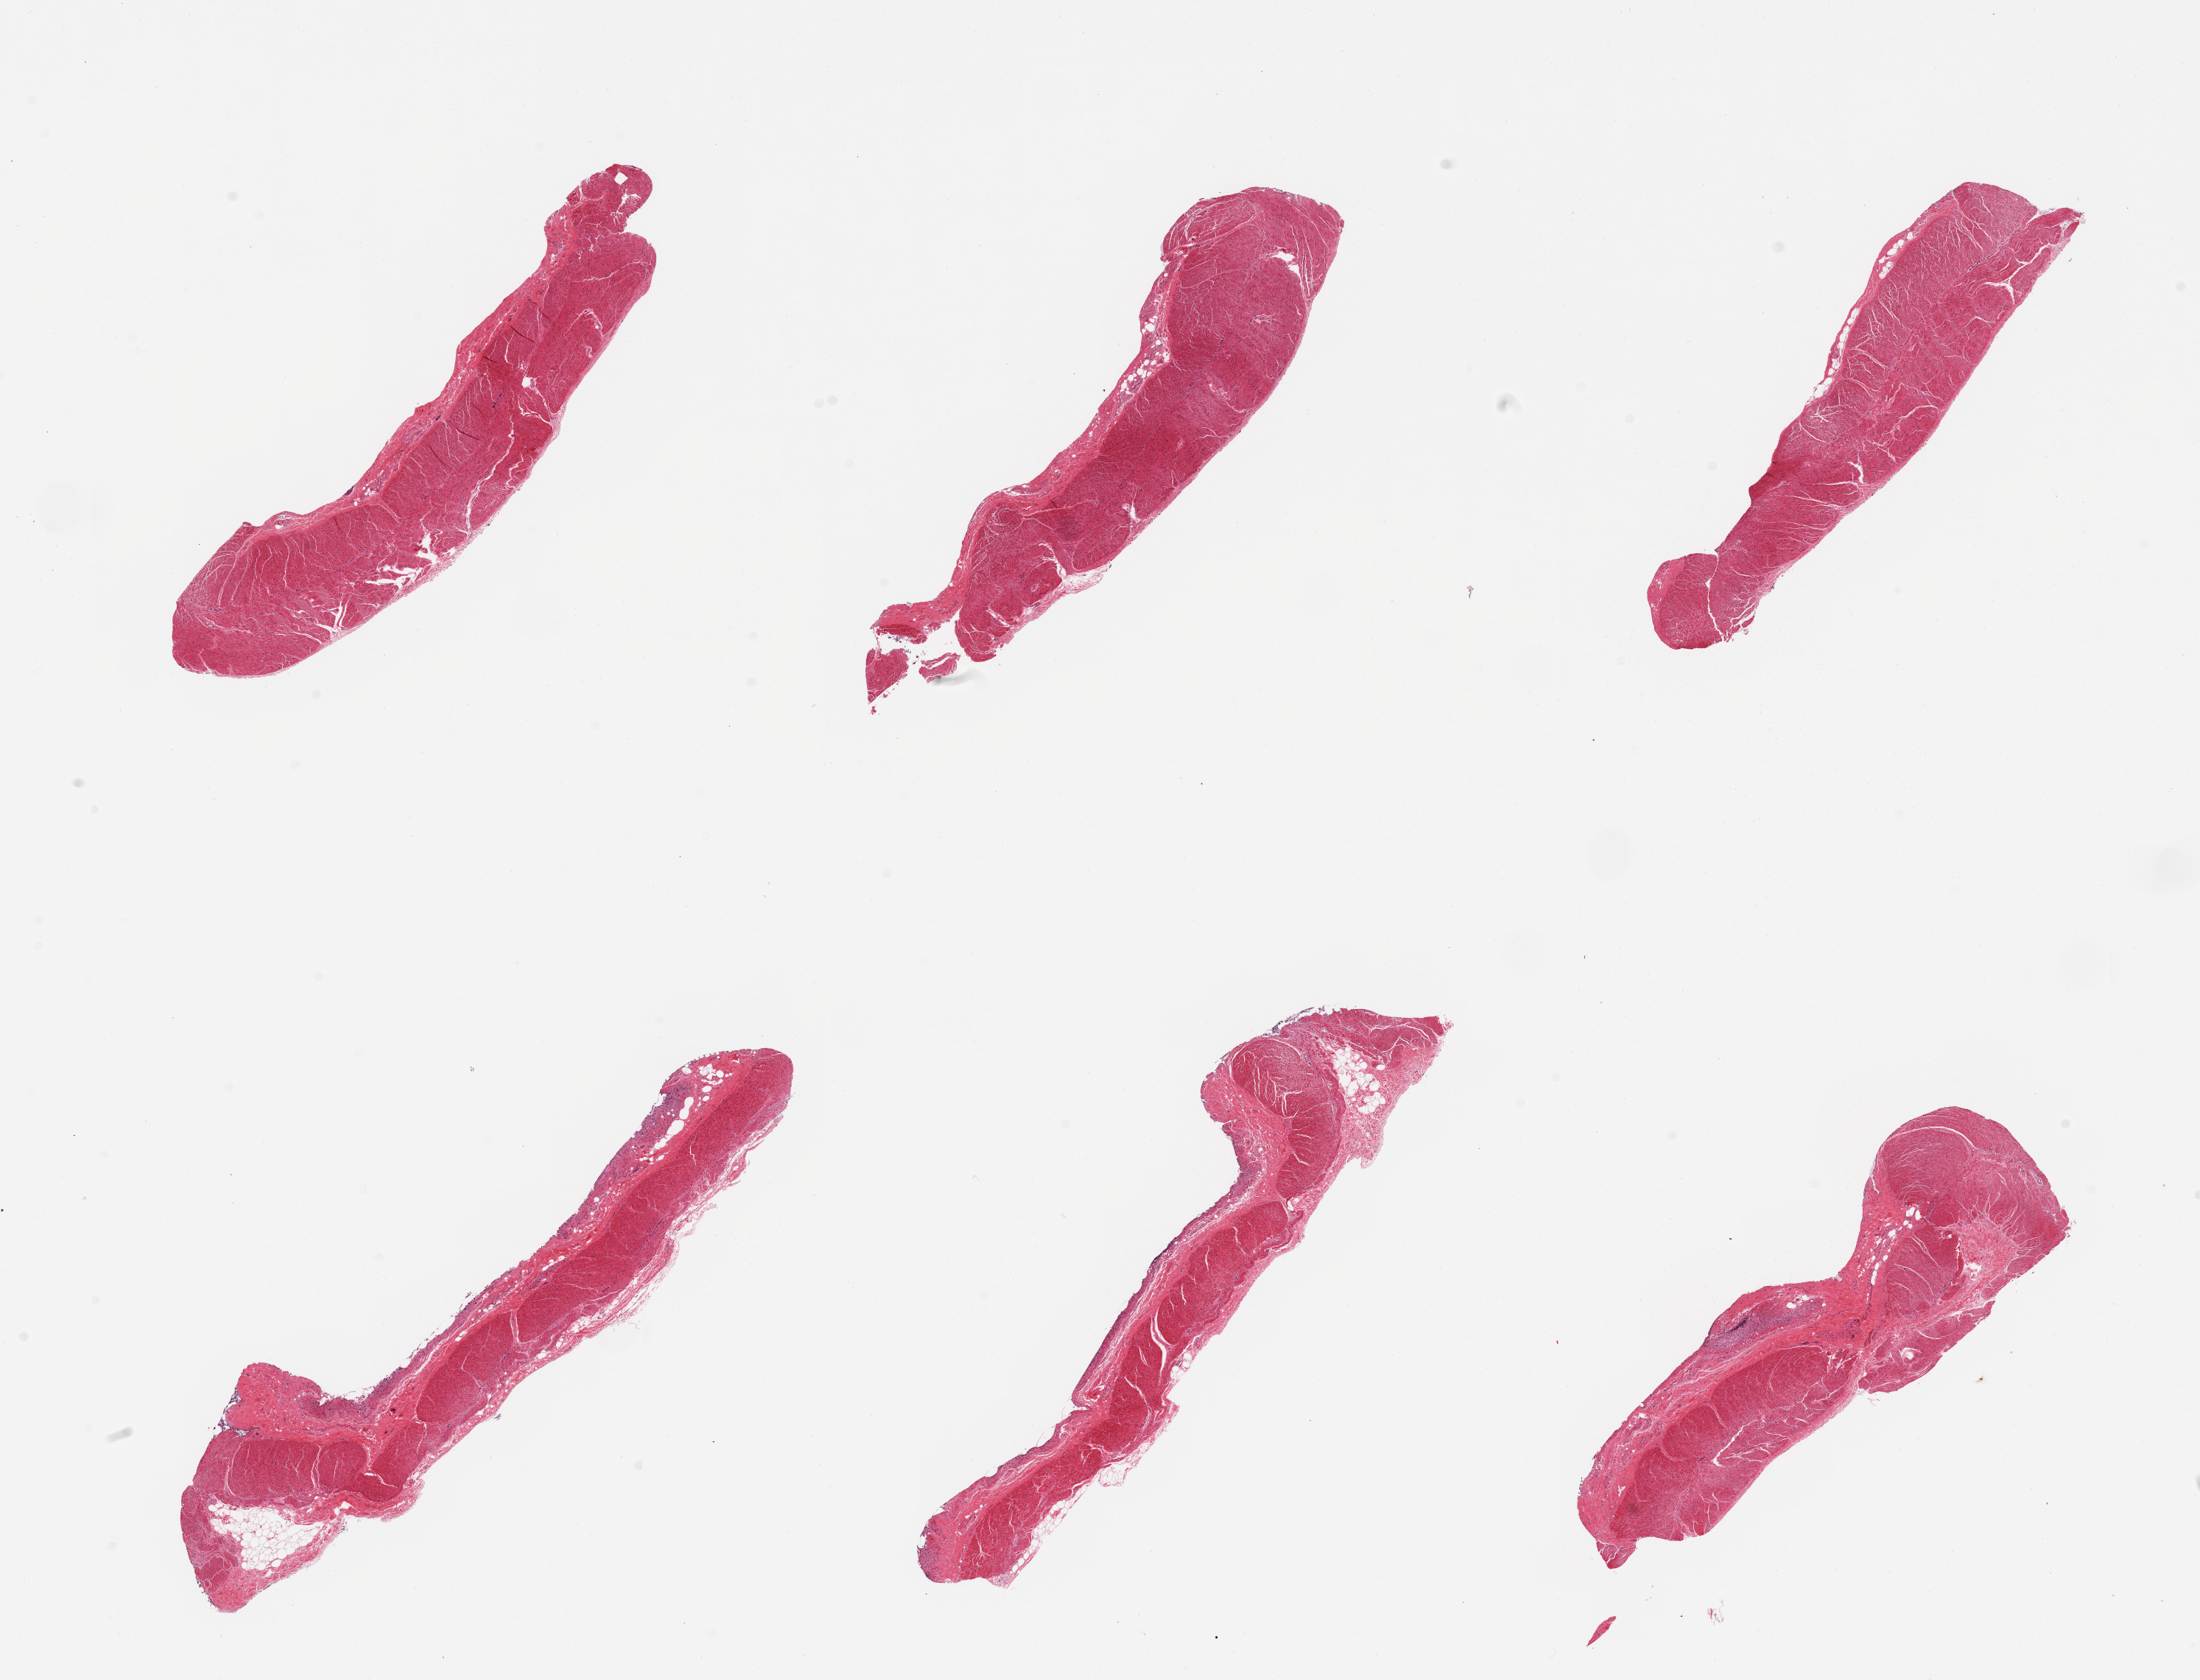
Hematoxylin and eosin (H&E) whole-slide image — shown as a low-resolution overview of the whole scanned area (about 23.6 x 18.0 mm, slide scanned at 20x); PAXgene-fixed, paraffin-embedded tissue; target tissue: sigmoid colon; tissue donor sample. Donor sex: female.
Pathologist's review note for this sample: 6 pieces, all muscularis.